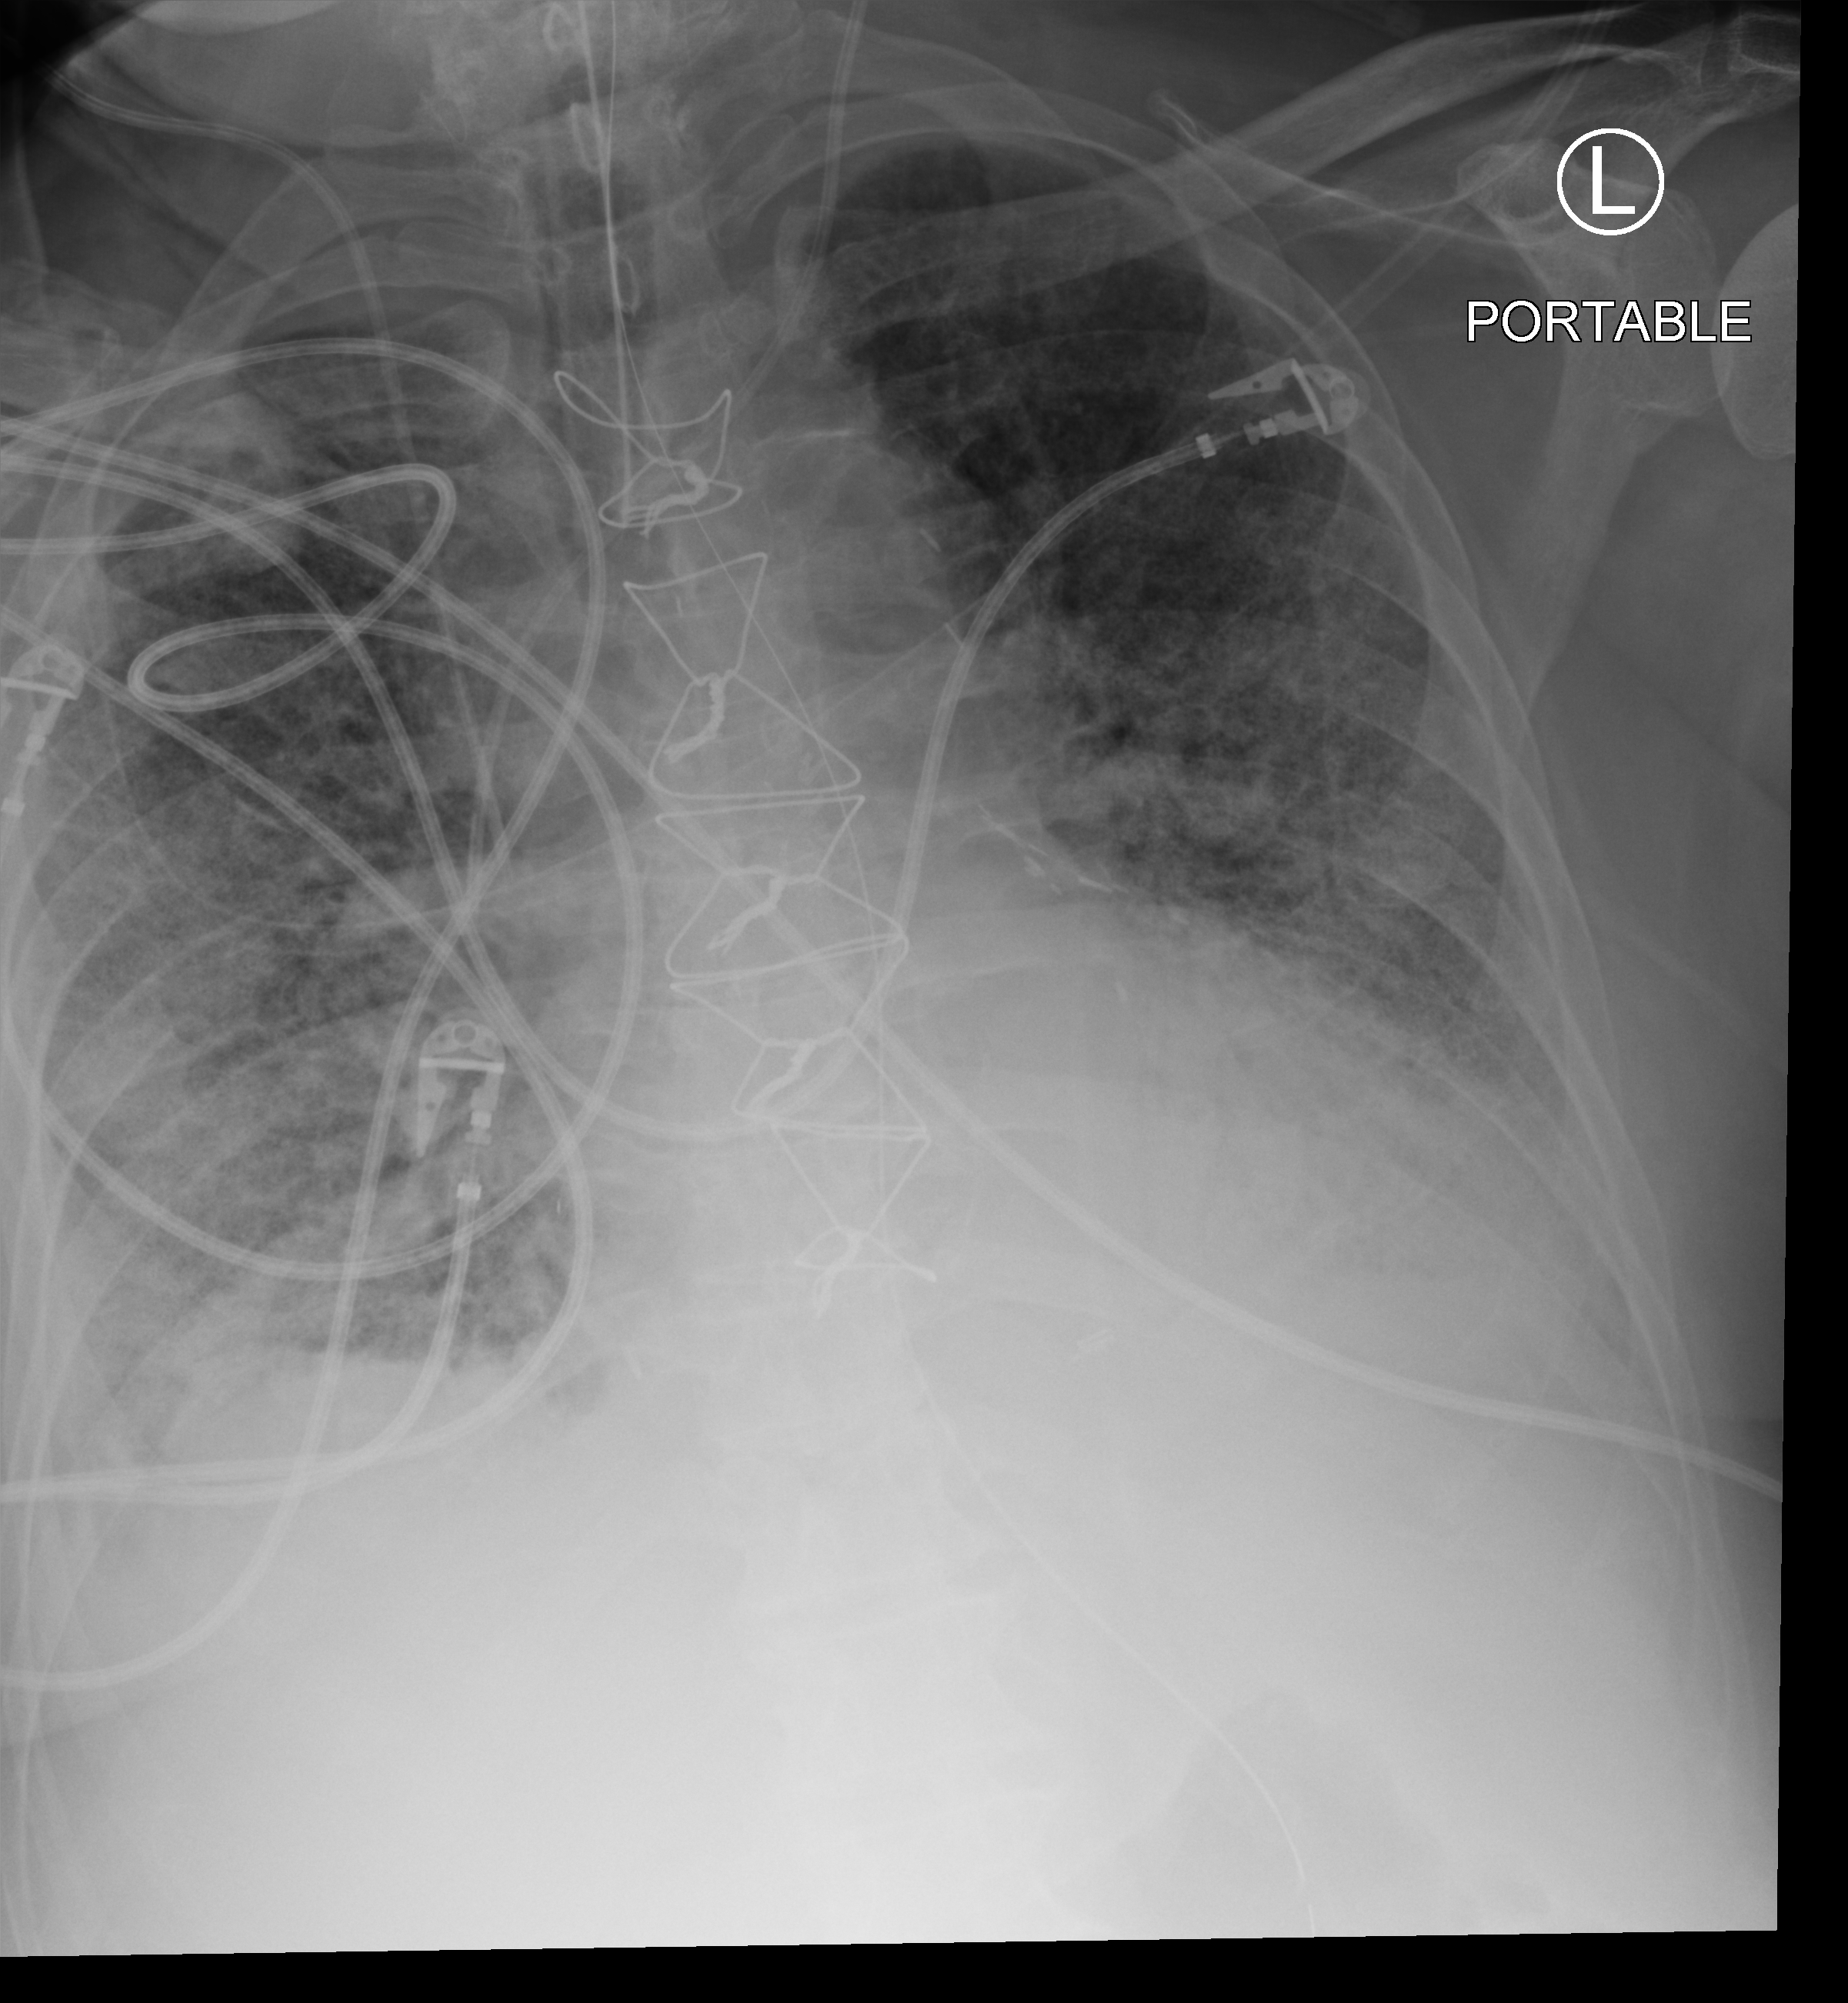
Bedside chest radiograph (computed radiography), anteroposterior (AP) projection. Male patient hospitalised with COVID-19, age 75–90 years.
Hospital-stay facts (about this admission, not read from this image; timing relative to this image not recorded):
- diabetes (admission record): no